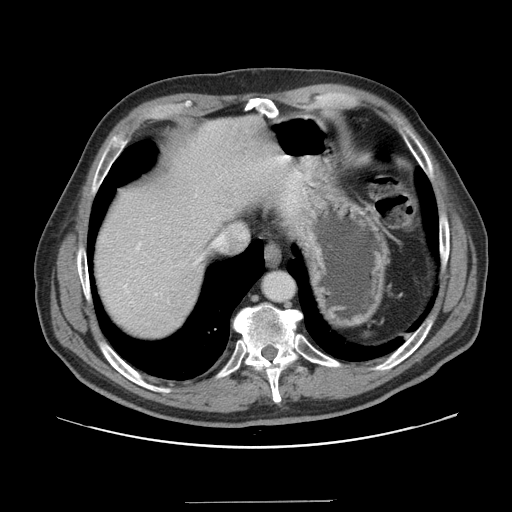
Contrast-enhanced abdominal CT, one axial slice; slice 135 of 151 in the series (ordered by position); 120 kVp; intravenous contrast given; soft-tissue window (W 400 / L 40 HU); 2.5 mm slice thickness; 512 × 512 image matrix, field of view 399 × 399 mm. Male patient, age 63 years. Case-level facts recorded for this patient, not image findings: diagnosis: colorectal cancer liver metastases, imaged before liver resection; multiple liver metastases: no; largest metastasis: 2.1 cm; chemotherapy before resection: no.
Annotated regions visible in this slice (outlined manually by an expert reader):
- hepatic veins: box from (x=217, y=236) to (x=224, y=244) px
- liver: (x=94, y=116)–(x=302, y=341)
- planned liver remnant (the part of the liver to remain after resection): (x=94, y=140)–(x=233, y=341)